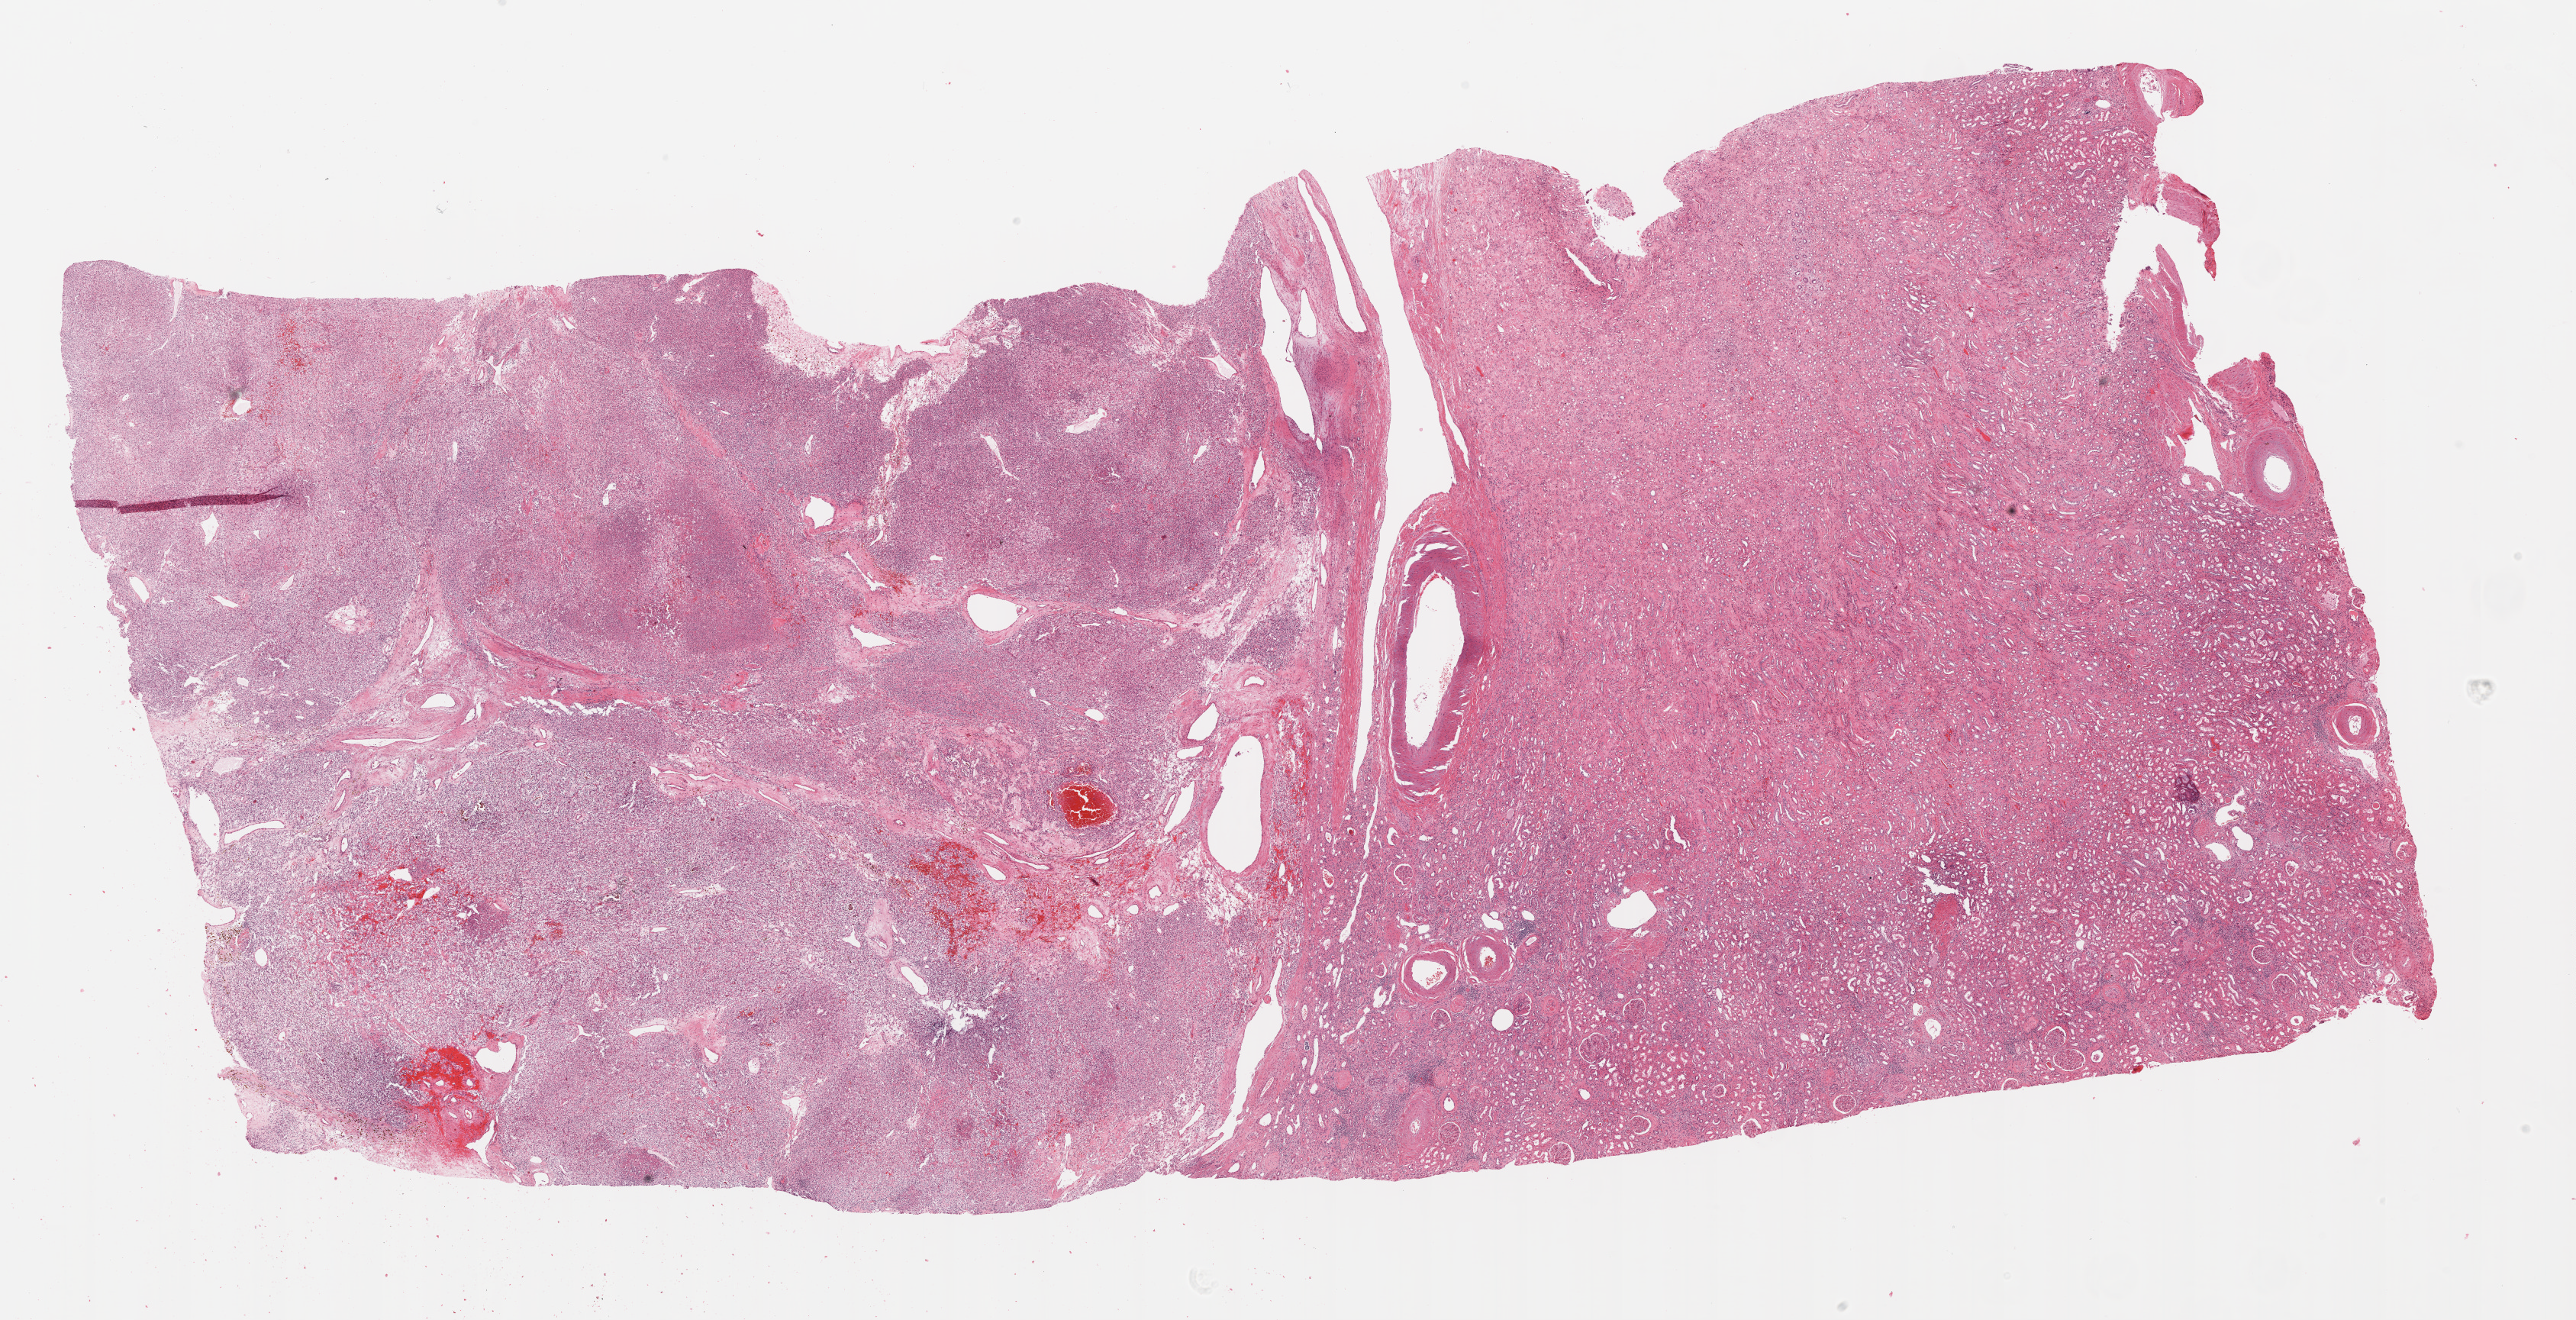
H&E whole-slide image — shown as a low-resolution overview of the whole scanned area (about 27.1 x 13.9 mm, slide scanned at 20x), formalin-fixed paraffin-embedded (FFPE) diagnostic section, kidney, primary tumour sample. Patient: male, age at initial diagnosis 63 years. Histologic grade: G2 (moderately differentiated).
AJCC pathologic stage: II. Pathologic diagnosis: Clear cell adenocarcinoma, NOS.